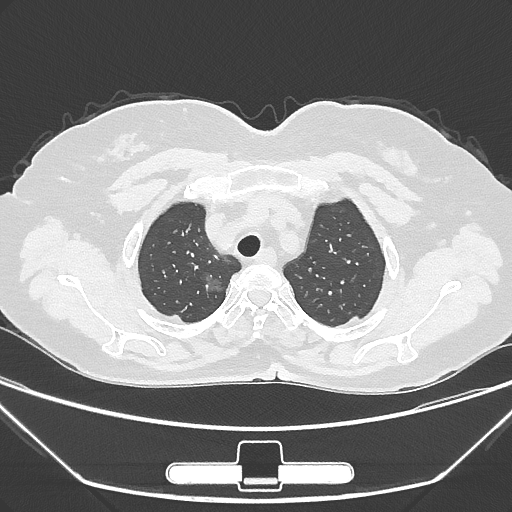
Chest CT, one axial slice; slice 234 of 275 in the series (ordered by position); reconstruction kernel IMR1,SharpPlus; 120 kVp; lung window (W 1500 / L -600 HU); 512 × 512 image matrix, field of view 356 × 356 mm. Female patient, age 63 years. Case-level facts recorded for this patient, not image findings: clinical TNM (as recorded): T1a N0 M0; histopathological grade: G1.
Outlined on this slice (bounding box drawn by a radiologist):
- lung tumour (recorded histology: adenocarcinoma): bounding box [x1, y1, x2, y2] px = [197, 268, 231, 302]